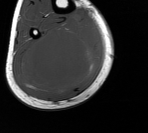
MRI of an extremity soft-tissue mass, one axial slice; MR volume resampled by the dataset authors to the PET/CT grid (not the native acquisition matrix); 3.27 mm slice thickness; 148 × 133 image matrix, field of view 145 × 130 mm. Male patient. From the clinical record (not read from this slice): histological type: liposarcoma - round cell; grade: high; site of the primary tumour: right calf.
Structures marked on this image (expert contour drawn on MRI and transferred to this co-registered scan by the dataset authors):
- gross tumour volume (mass): bounding box <13,18,103,97> (left, top, right, bottom; pixels)